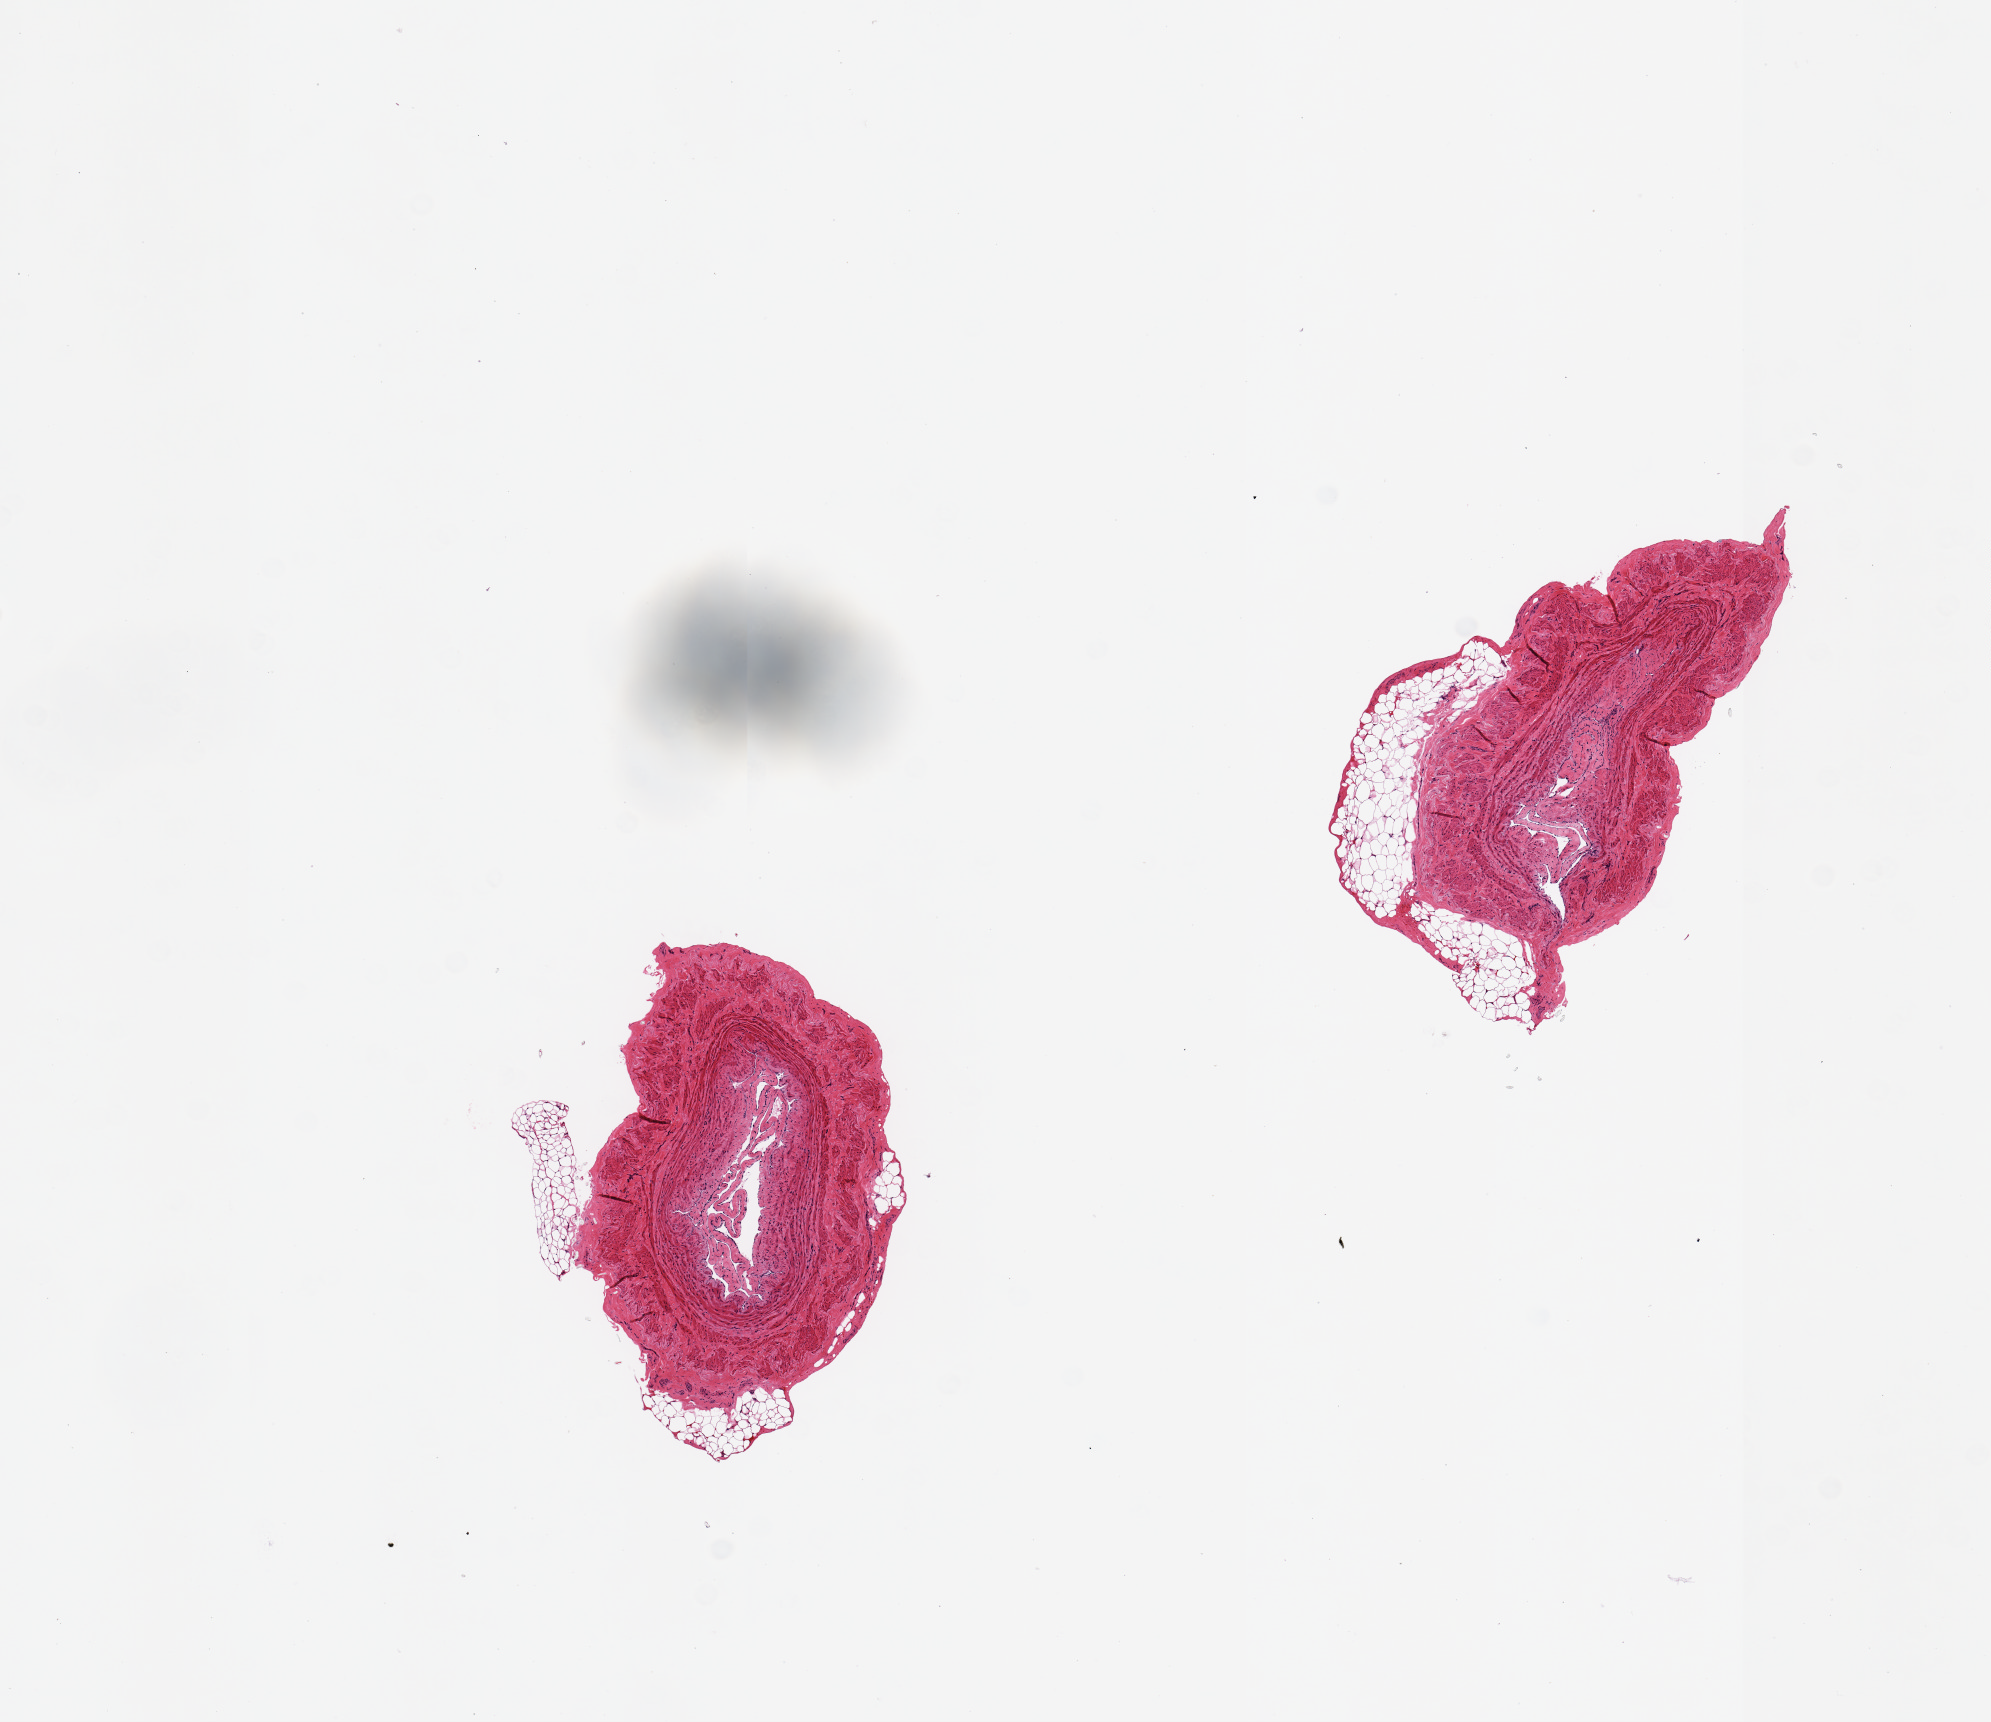
Digitized haematoxylin and eosin-stained section, shown as a low-resolution overview of the whole scanned area (about 7.9 x 6.8 mm, slide scanned at 20x); PAXgene-fixed, paraffin-embedded tissue; target tissue: tibial nerve; tissue donor sample. Donor sex: male.
• review note (as recorded): 2 pieces; non target vessels with attached 20-25% fat; target nerve not present